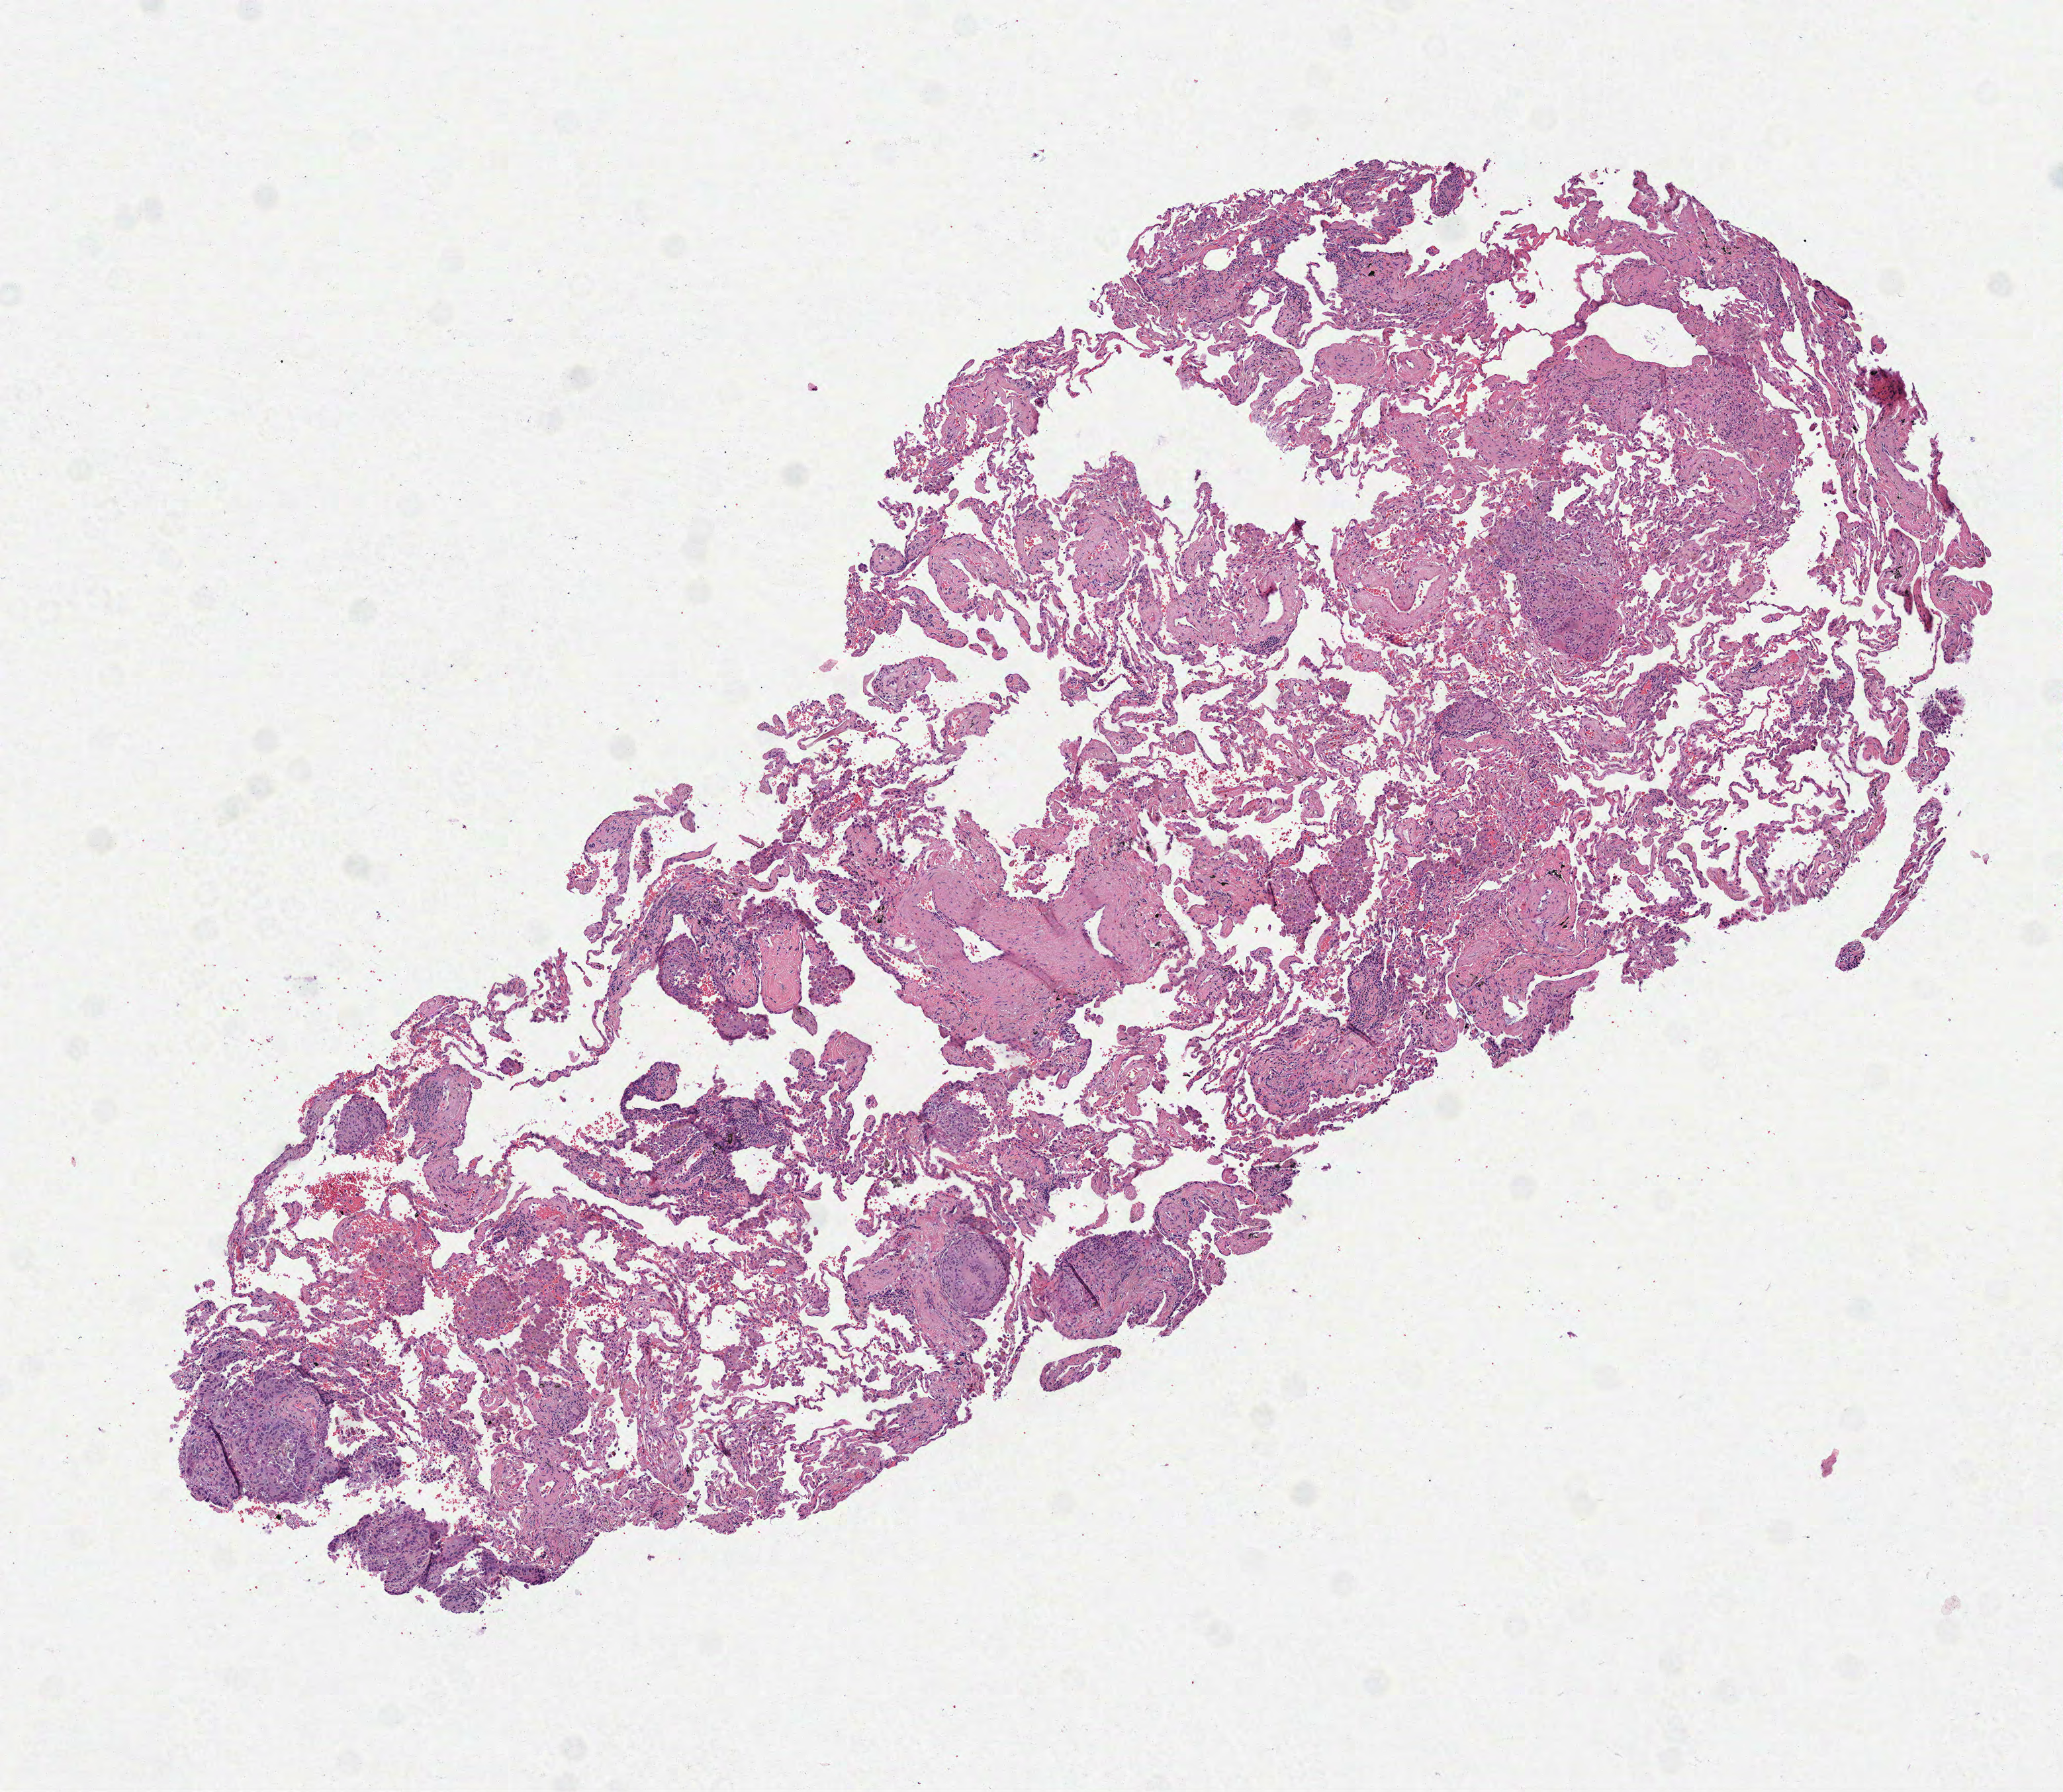
Whole-slide histology image, H&E — low-resolution overview of the scanned area, about 6.3 x 5.5 mm, formalin-fixed paraffin-embedded (FFPE) diagnostic section, primary tumour sample from the lung. Male, age 69 years at initial diagnosis.
AJCC pathologic stage: IA (7th edition). Pathologic diagnosis: Squamous cell carcinoma, NOS. Laterality: right.